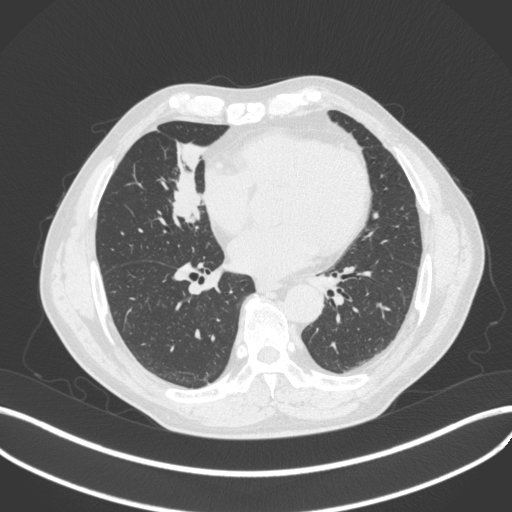
Chest CT, one axial slice; position 167 of 429 along the scan axis; 120 kVp; lung window (W 1500 / L -600 HU); 512 × 512 image matrix, field of view 400 × 400 mm. Patient: male, 61 years. Case-level facts recorded for this patient, not image findings: clinical TNM (as recorded): T2b N1 M0.
Structures marked on this image (rectangle marked by the reading radiologist):
- lung tumour (recorded histology: squamous cell carcinoma): bounding box <169,161,209,227> (left, top, right, bottom; pixels)